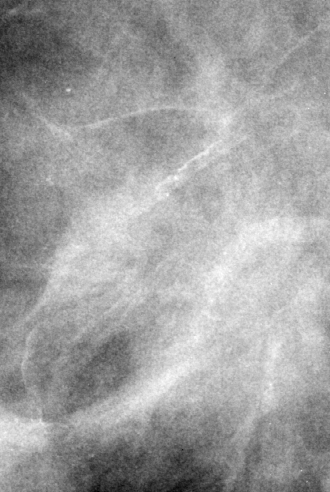
Crop from a digitized film mammogram around one marked abnormality; right breast; MLO view.
Marked abnormality: mass, shape architectural distortion, margins spiculated; BI-RADS assessment category 5; pathology result (as recorded, not read from the image): malignant.